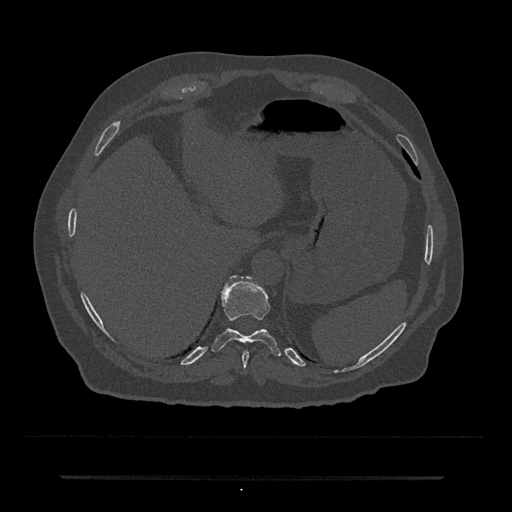
CT including the spine, one axial slice. Slice 232 of 797 in the series (ordered by position). Reconstruction kernel Br40s/3. 120 kVp. Bone window (W 1800 / L 400 HU). 0.5 mm slice thickness. 512 × 512 image matrix, field of view 437 × 437 mm. Patient: male, 69 years. From the clinical record (not read from this slice): primary cancer: prostate.
Outlined on this slice (semi-automatically segmented with operator editing):
- T10 vertebra: bounding box [x1, y1, x2, y2] px = [212, 275, 281, 357]
- T11 vertebra: [230, 275, 243, 280]
- T9 vertebra: [242, 350, 249, 368]